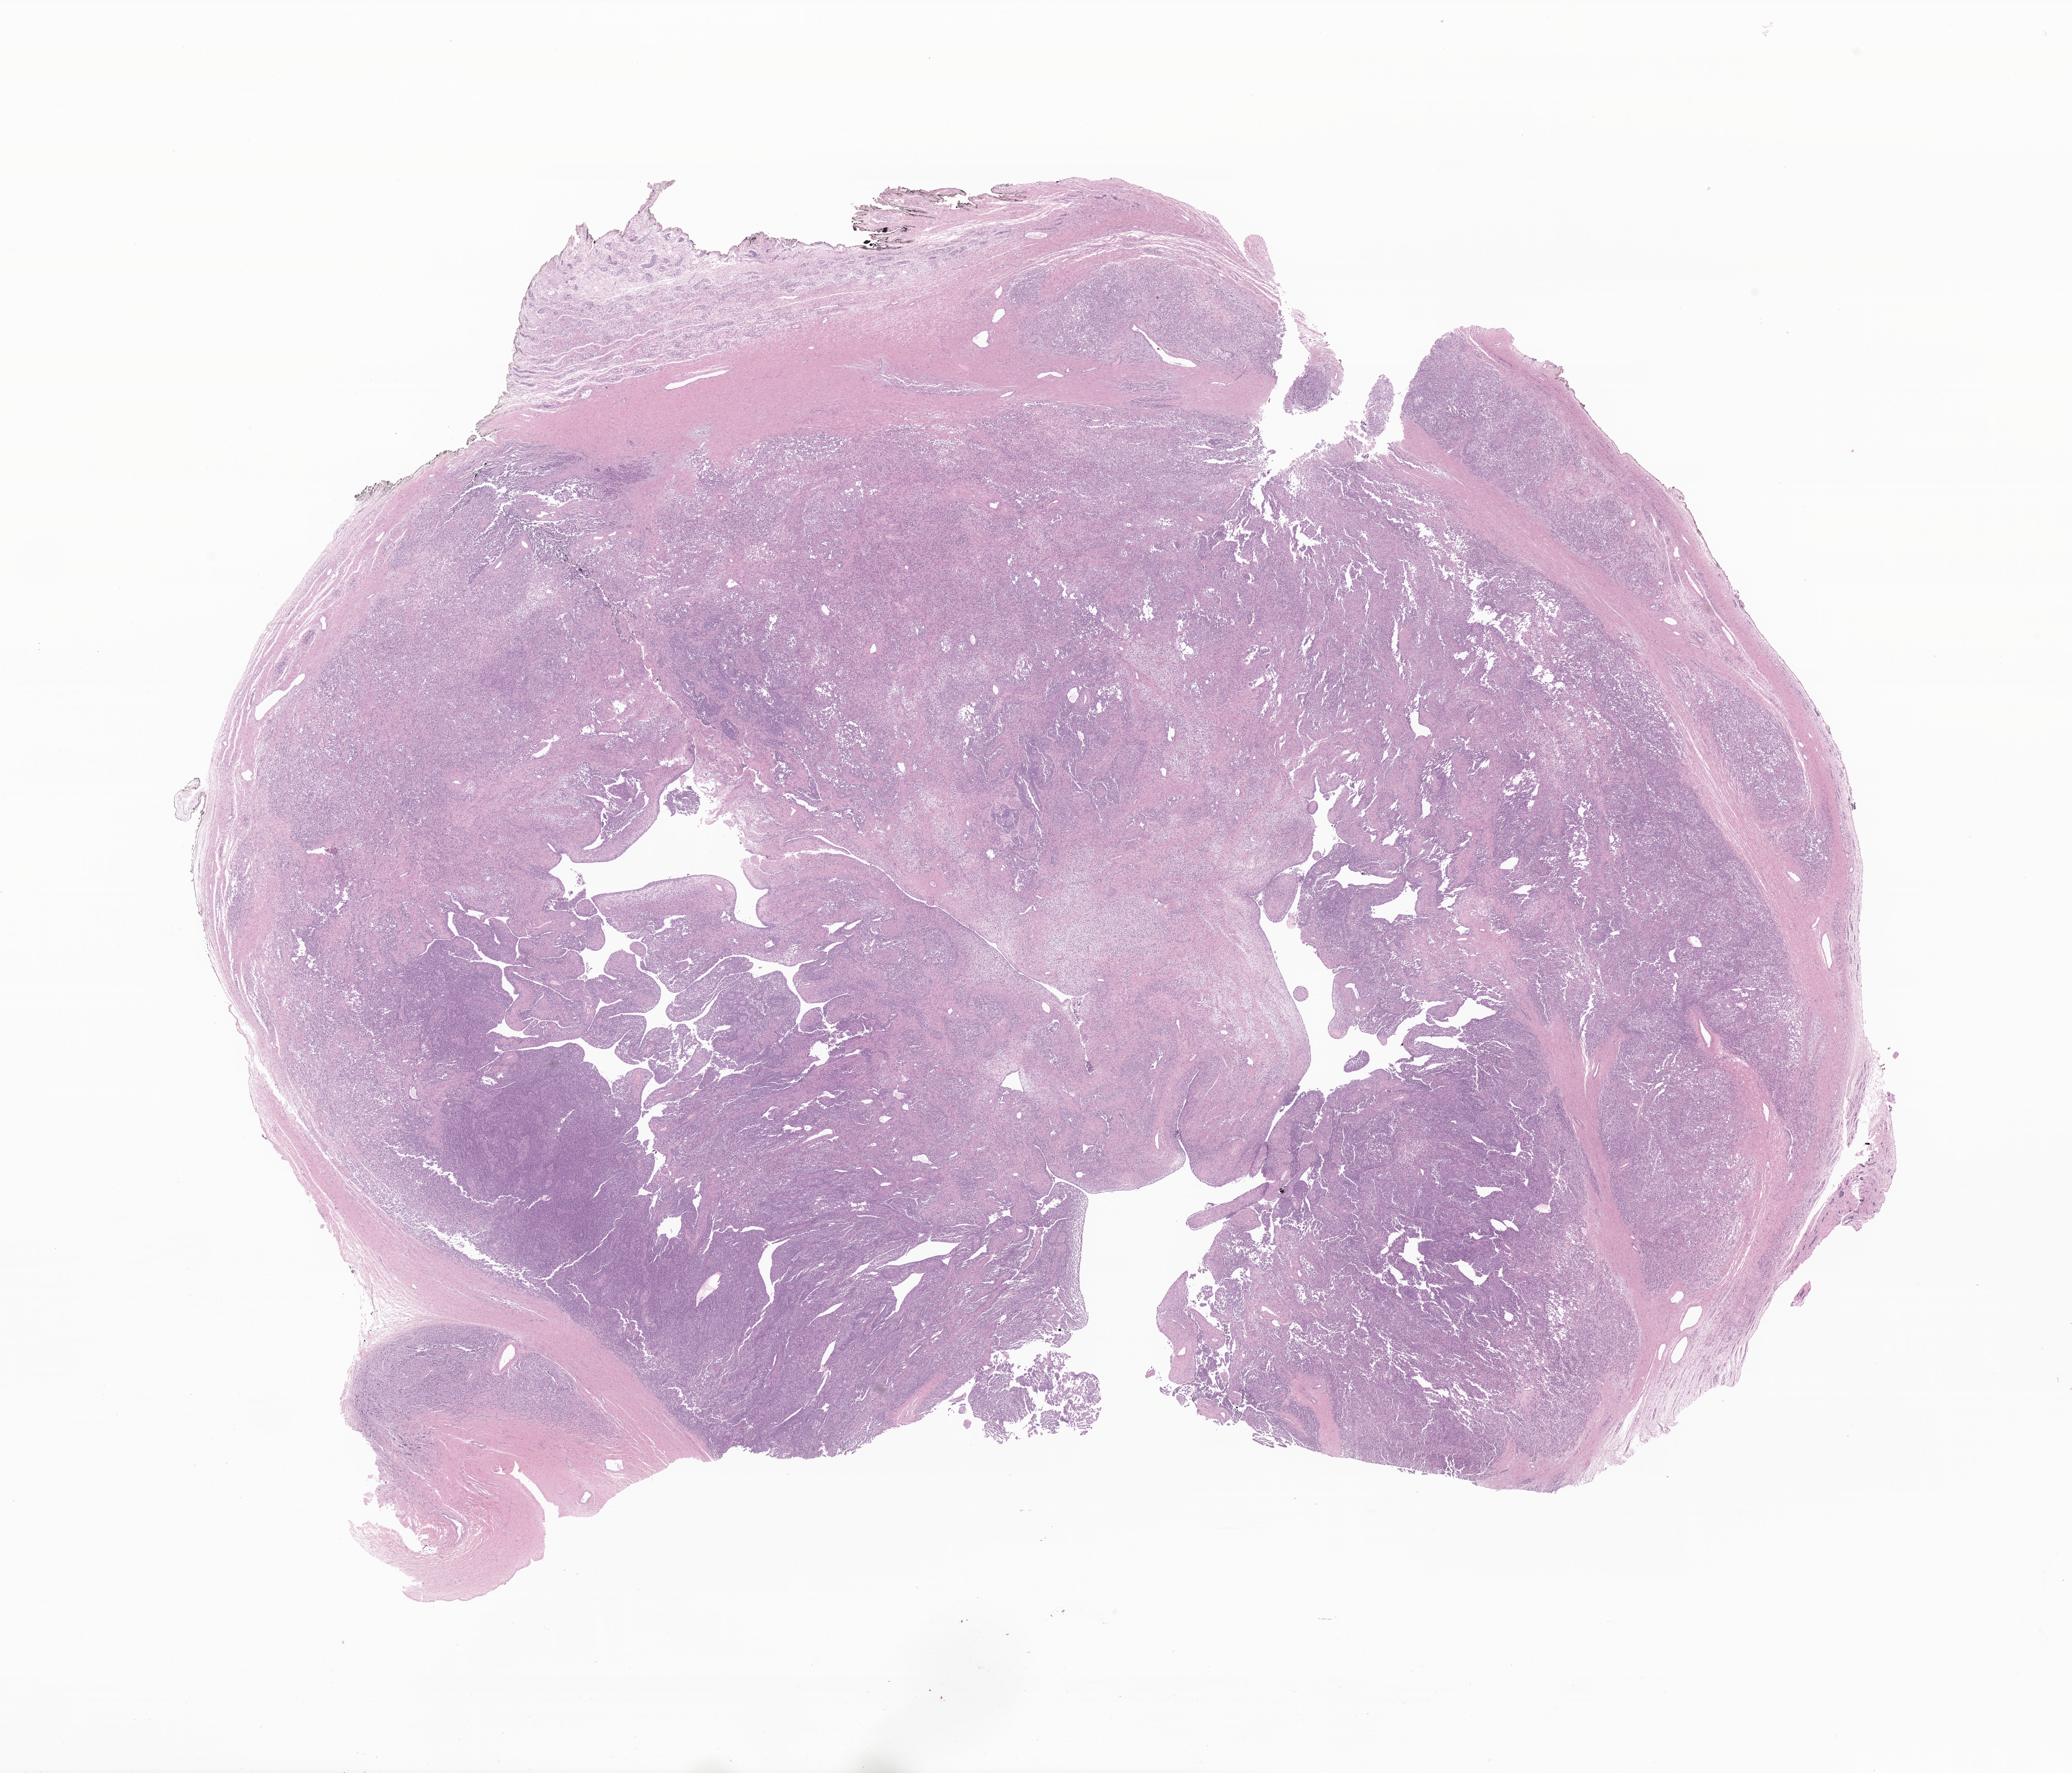
Whole-slide image, H&E stain of tumor tissue from the testis — low-resolution overview of the scanned area, about 22.0 x 18.8 mm; formalin-fixed paraffin-embedded section. Male patient, age 33 months (2 years 9 months).
Recorded diagnosis: Sex cord-gonadal stromal tumor, NOS.